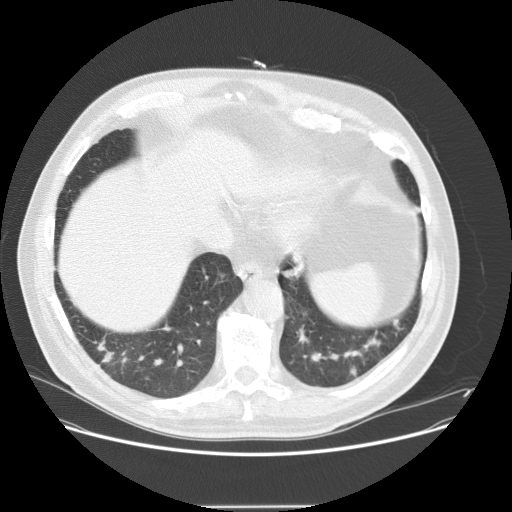
Chest CT (low-dose screening protocol), one axial image. Baseline annual screen. Lung window (W 1500 / L -600 HU). Standard (soft-tissue) reconstruction kernel (STANDARD). 512 × 512 image matrix, field of view 400 × 400 mm. Male, age 61 years at enrolment. Current smoker at enrolment.
Expert reader's lesion annotation, bounding box <89,330,142,382> (left, top, right, bottom; pixels). The screening reader recorded 2 non-calcified nodules or masses ≥4 mm on this exam (left lower lobe, right lower lobe); which of them this box marks is not recorded.